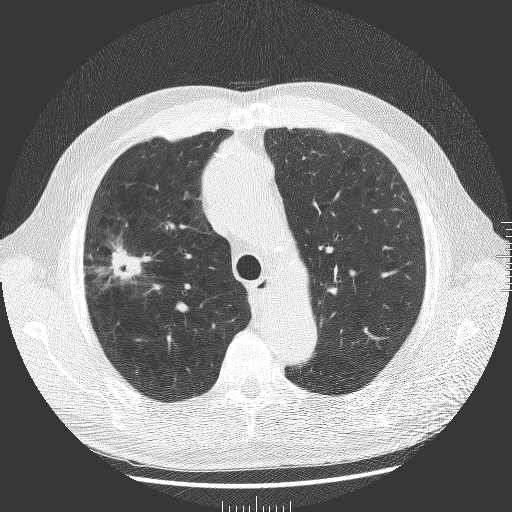
Low-dose screening chest CT, one axial slice; position 136 of 181 along the scan axis; reconstruction kernel BONE; lung window (W 1500 / L -600 HU); 2 mm slice thickness; 512 × 512 image matrix, field of view 380 × 380 mm.
Structures marked on this image (expert manual segmentation):
- lesion 1 (tumor, upper lobe of right lung): box from (x=109, y=243) to (x=142, y=282) px